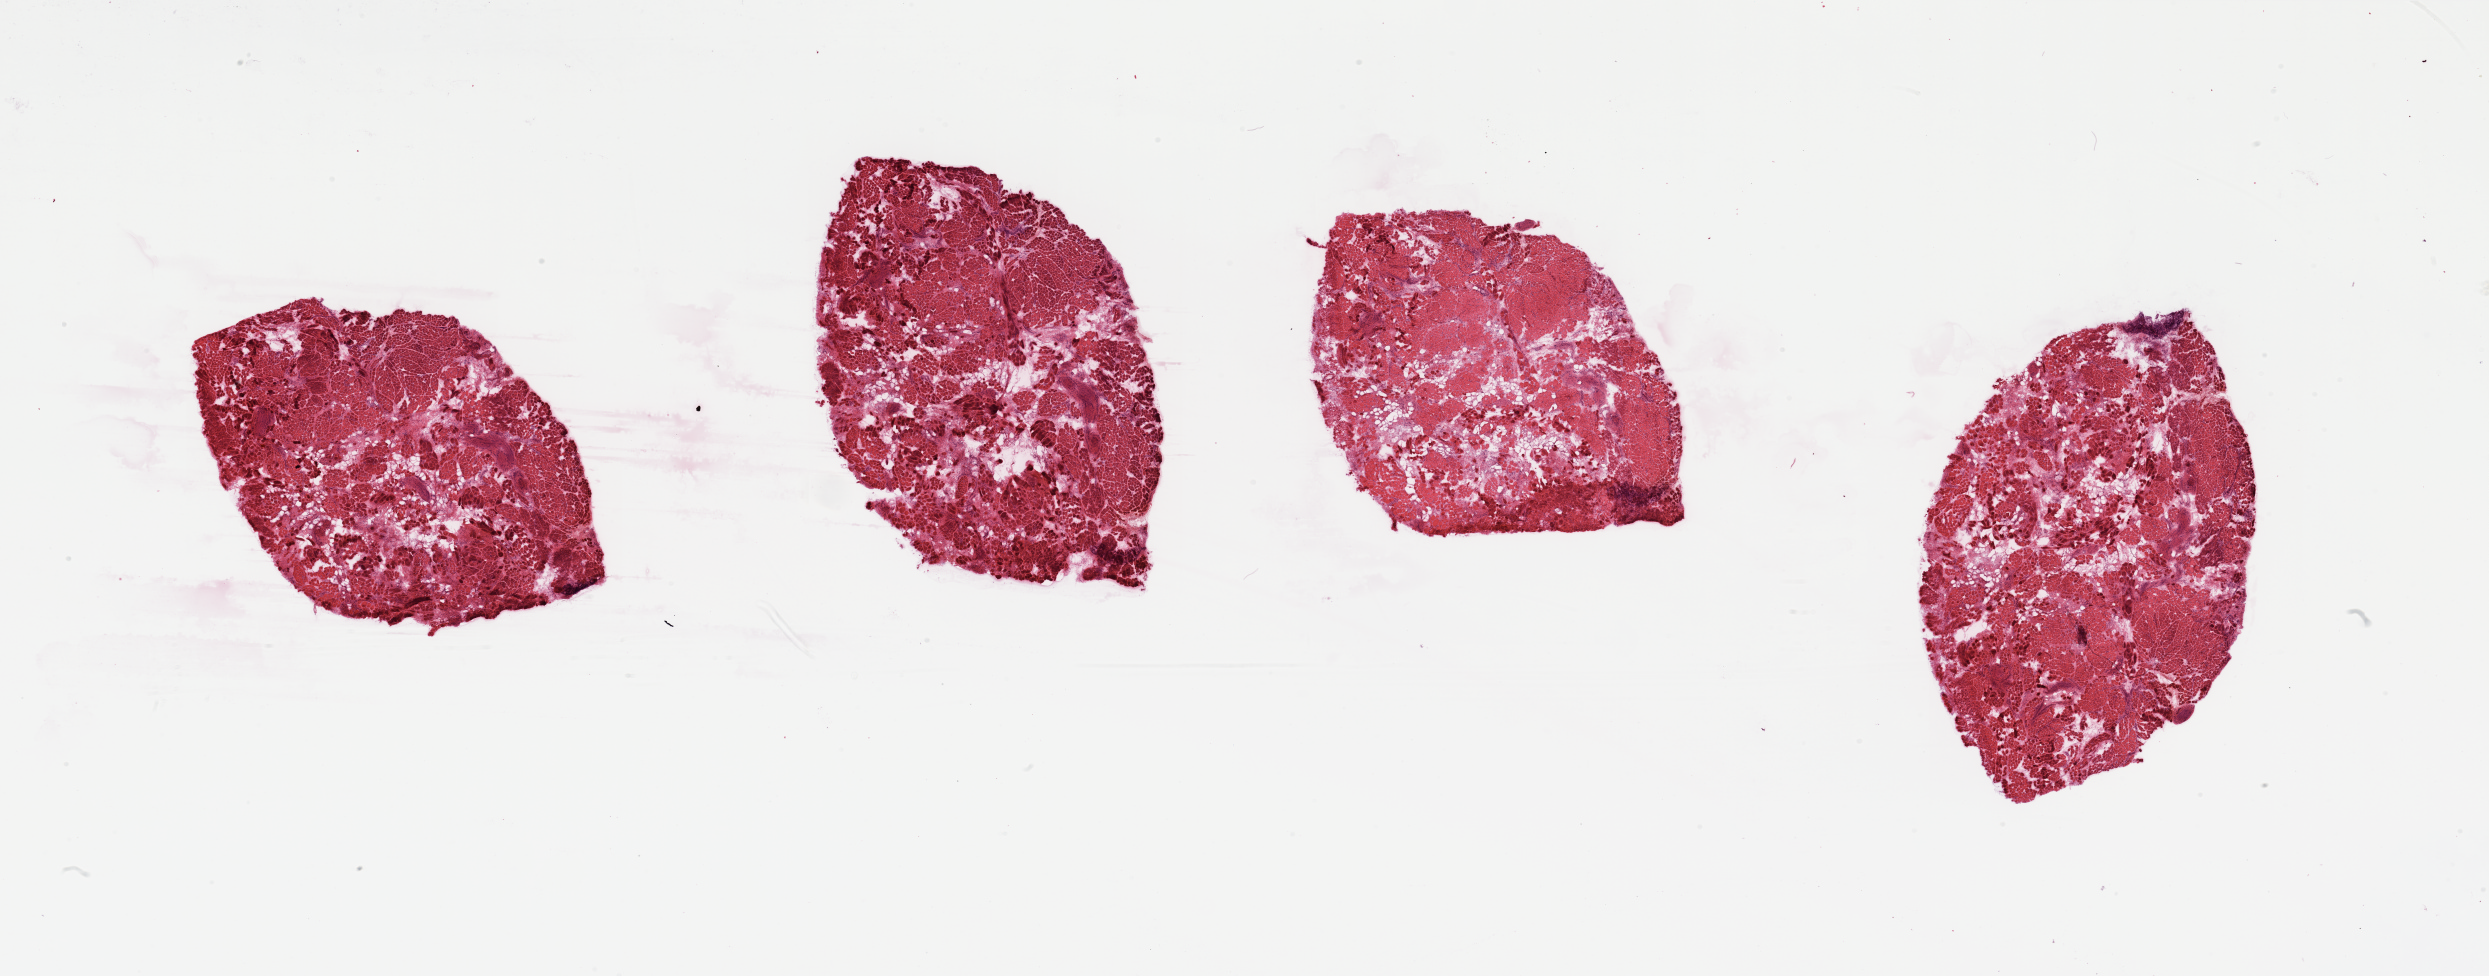
Digitized Hematoxylin and eosin (H&E) stained tissue section (whole slide) — low-resolution overview of the scanned area, about 39.4 x 15.4 mm (from a 20x scan). Head and neck, tissue type not recorded. Male, 54 y/o.
* patient diagnosis: Squamous cell carcinoma, NOS